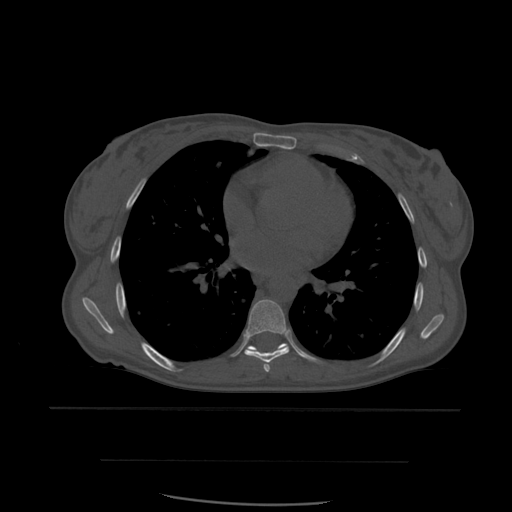
CT including the spine, one axial slice; slice 370 of 574 in the series (ordered by position); bone window (W 1800 / L 400 HU); 1.25 mm slice thickness; 512 × 512 image matrix. Patient age 48 years. Case-level facts recorded for this patient, not image findings: primary cancer: lung.
Annotated regions visible in this slice (semi-automatic segmentation, software-assisted and operator-edited):
- T6 vertebra: bounding box [x1, y1, x2, y2] px = [264, 365, 270, 372]
- T7 vertebra: [244, 300, 290, 372]
- T8 vertebra: [247, 343, 288, 352]